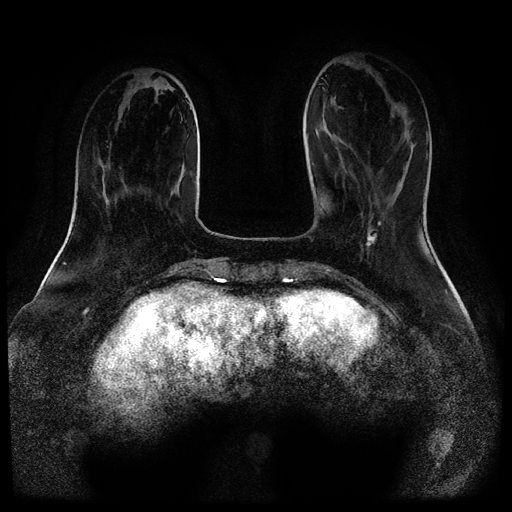
Breast MRI (dynamic contrast-enhanced, multi-phase), one axial slice. Slice 30 of 116 in the series (ordered by position). Dynamic contrast-enhanced series, time point 2 of 5 at this slice position (early post-contrast). 1.5 T. TE 2.6 ms, TR 5.3 ms. 512 × 512 image matrix, field of view 360 × 360 mm. Patient: female, 52 years.
Outlined on this slice (semi-automatically segmented with operator editing):
- breast lesion (labelled 'tumour' in the annotation; benign lesions carry a separate 'benign' label): bounding box [x1, y1, x2, y2] px = [365, 222, 381, 247]